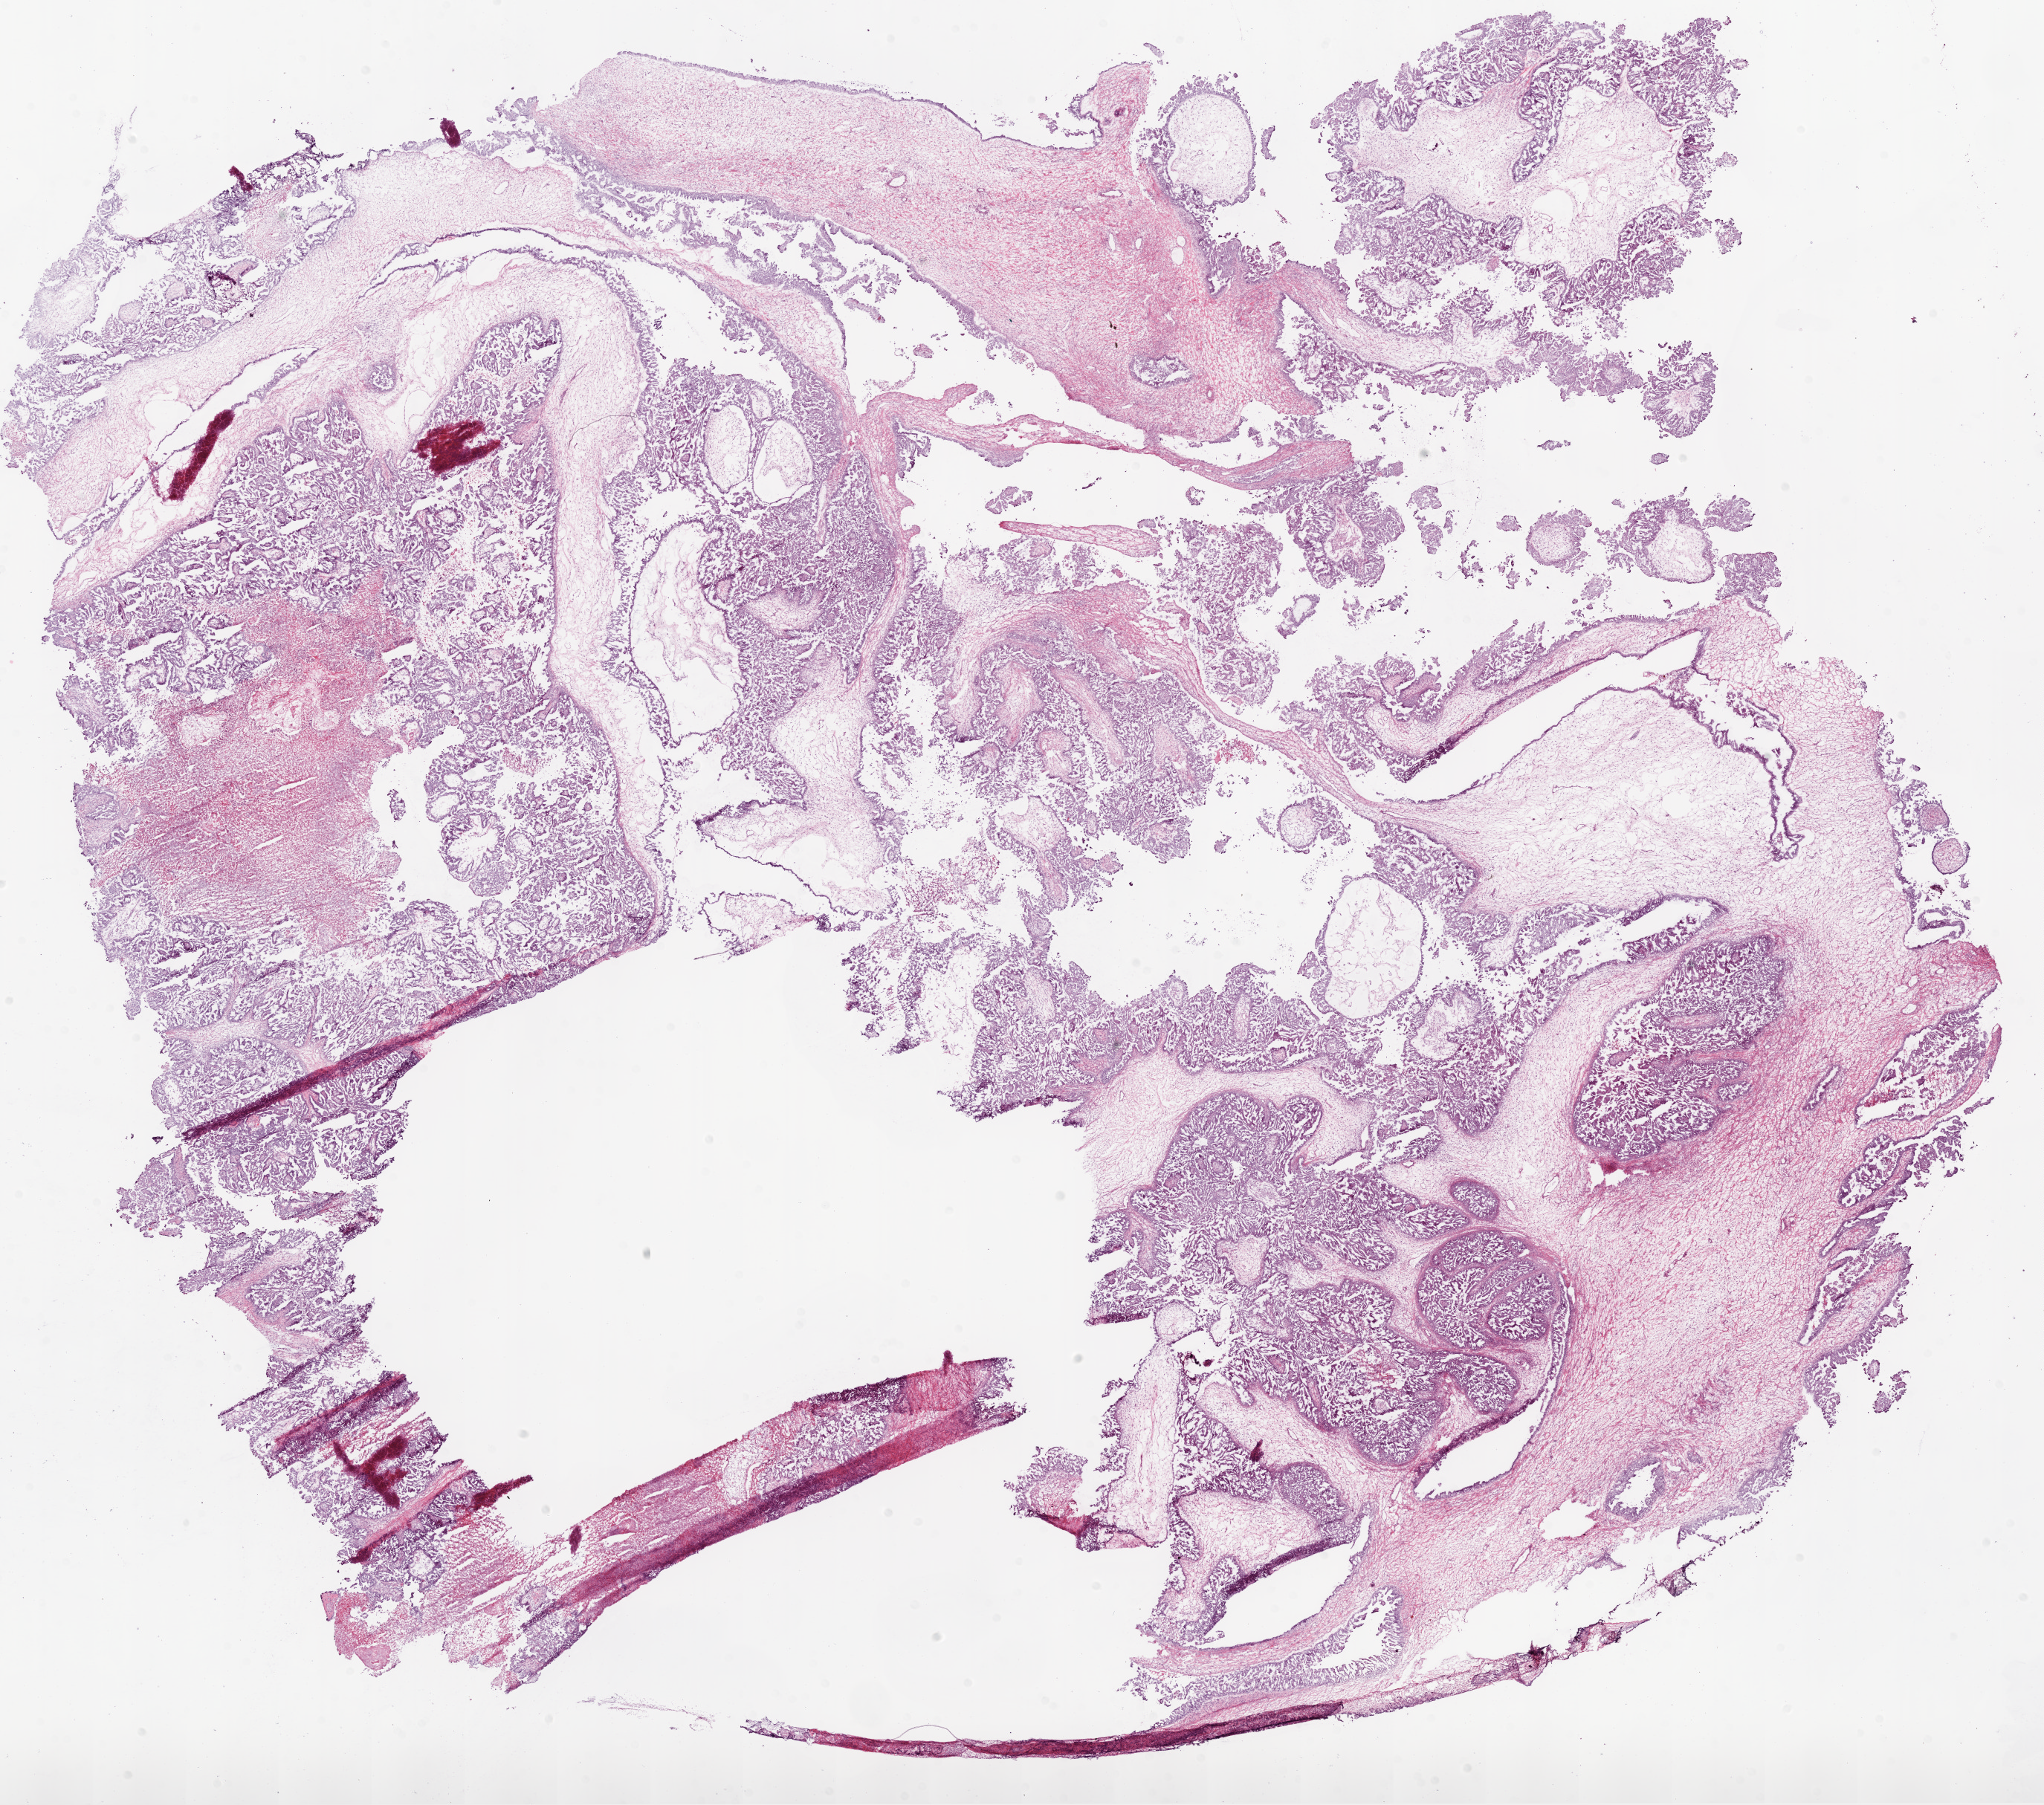
H&E-stained whole-slide image — a low-resolution overview of the entire scanned area, about 22.1 x 19.5 mm, frozen section from the bottom of the tissue portion, ovary, primary tumour sample. Female patient; age at initial diagnosis 73 years. Histologic grade: G3 (poorly differentiated). Pathologist review of this section (percent, as recorded): tumour cells 80%, tumour nuclei 90%, normal cells 0%, stromal cells 10%, necrosis 10%.
- laterality: bilateral
- histologic diagnosis: Serous cystadenocarcinoma, NOS
- FIGO stage: IIIC